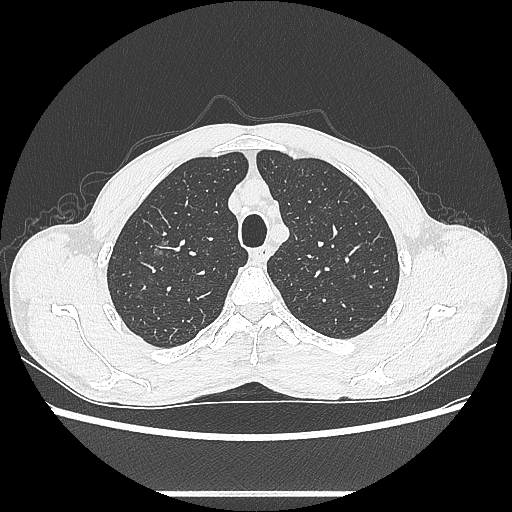
Chest CT, one axial slice. Reconstruction kernel LUNG. Lung window (W 1500 / L -600 HU). 0.62 mm slice thickness. 512 × 512 image matrix, field of view 357 × 357 mm. Patient: male, 54 years. From the clinical record (not read from this slice): clinical TNM (as recorded): T1a N0 M0.
Outlined on this slice (bounding box drawn by a radiologist):
- lung tumour (recorded histology: adenocarcinoma): bounding box <147,233,178,273> (left, top, right, bottom; pixels)